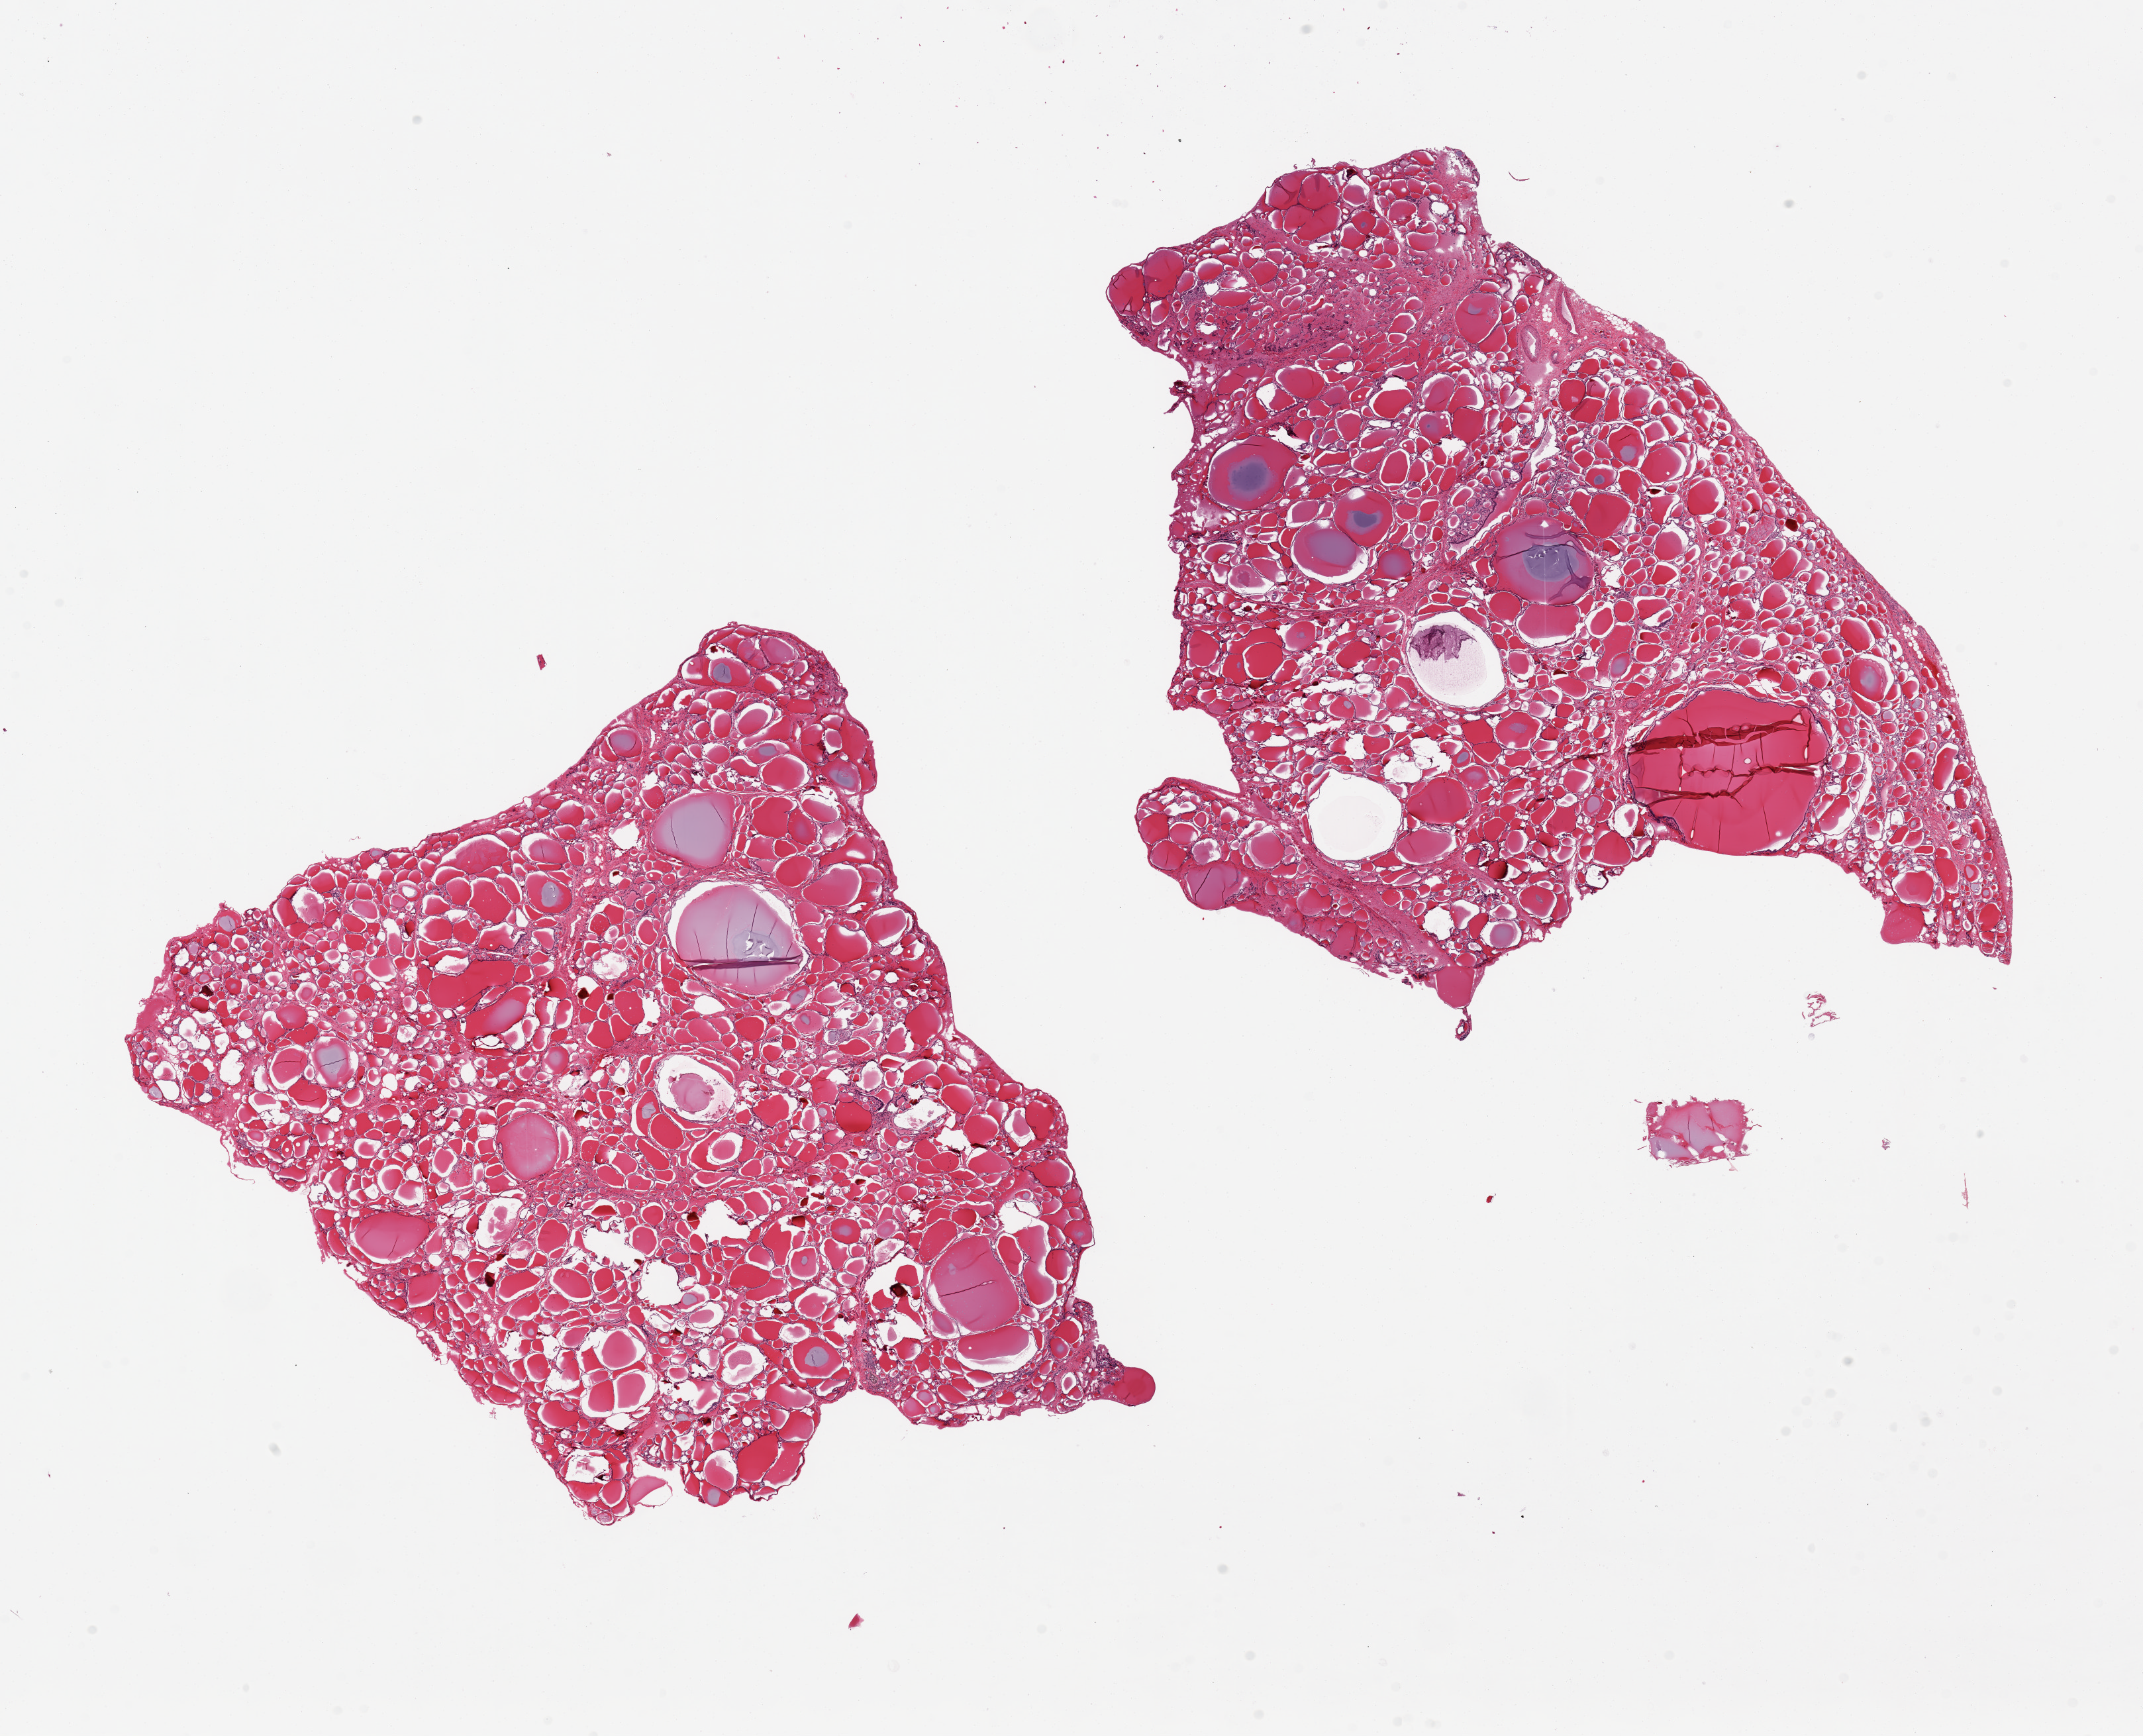
Digitized haematoxylin and eosin-stained section, brightfield — shown as a low-resolution overview of the whole scanned area (about 25.6 x 20.7 mm, from a 20x scan); PAXgene-fixed paraffin-embedded (PFPE) section; target tissue: thyroid; donor tissue sample.
Pathologist's review note for this sample: 2 pieces, 11x10 & 12.5x9mm; multiple small (1-2mm) colloid cysts.